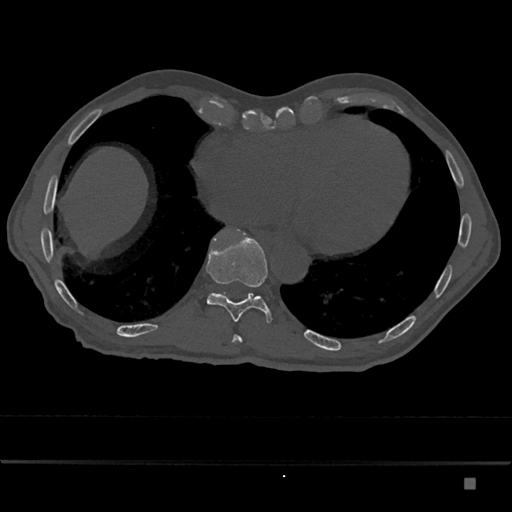
CT including the spine, one axial slice. Reconstruction kernel Br40s/3. 120 kVp. Bone window (W 1800 / L 400 HU). 512 × 512 image matrix, field of view 390 × 390 mm. Patient: male, 72 years. Case-level facts recorded for this patient, not image findings: primary cancer: prostate.
Annotated regions visible in this slice (semi-automatically segmented with operator editing):
- T10 vertebra: box from (x=206, y=230) to (x=272, y=323) px
- T9 vertebra: (x=232, y=335)–(x=242, y=342)